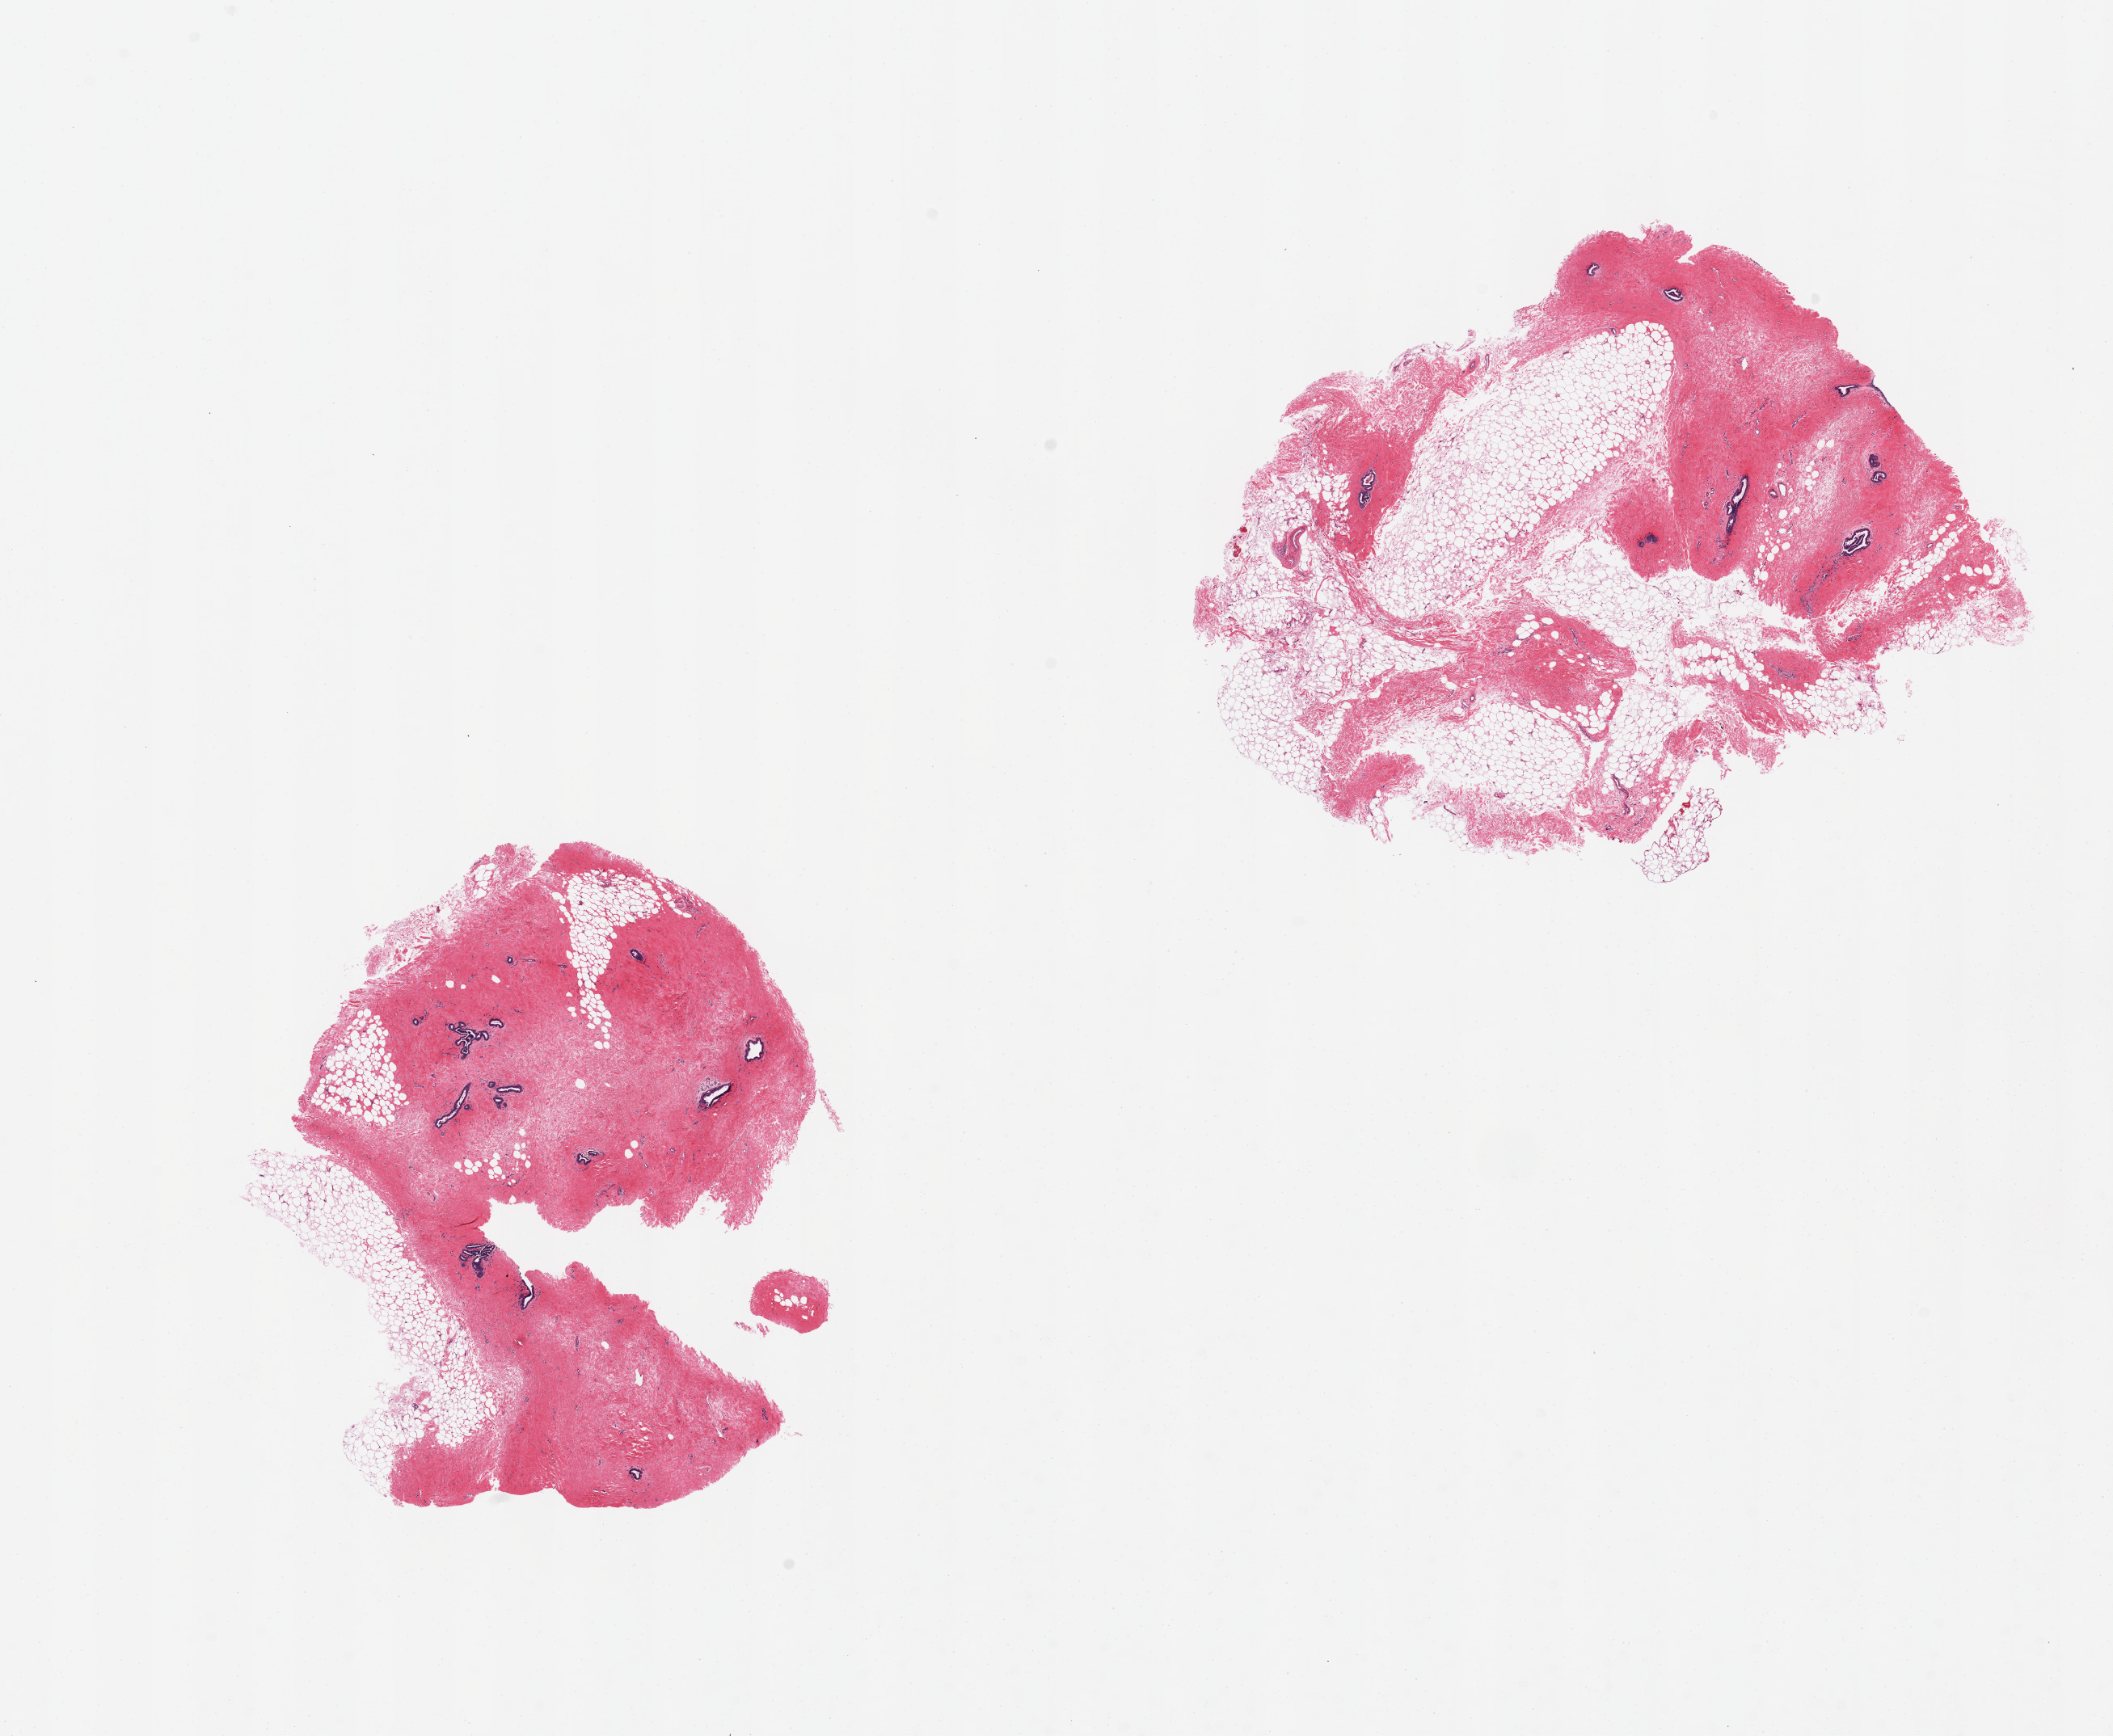
Digitized hematoxylin and eosin (H&E)-stained section — a low-resolution overview of the entire scanned area, about 20.7 x 17.0 mm; PAXgene-fixed paraffin-embedded (PFPE) section; target tissue: breast; tissue donor sample. Donor: male.
Pathologist's review note for this sample: 2 pieces; stromal and ductal gynecomastoid hyperplasia; about 50% fat.